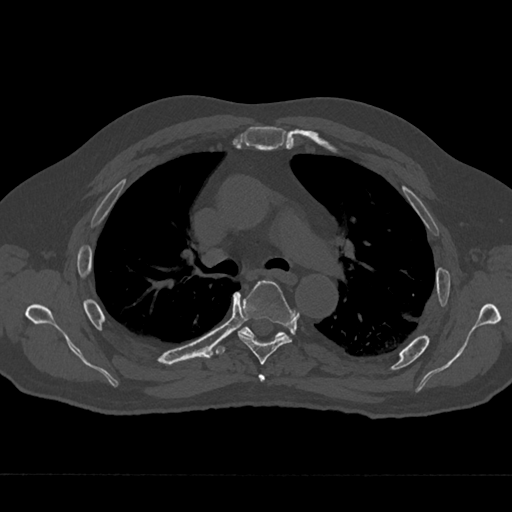
CT including the spine, one axial slice; slice 460 of 797 in the series (ordered by position); 120 kVp; bone window (W 1800 / L 400 HU); 0.5 mm slice thickness; 512 × 512 image matrix, field of view 377 × 377 mm. Patient: male, 75 years. From the clinical record (not read from this slice): primary cancer: renal; vertebrae with lytic lesions (as recorded): T4.
Structures marked on this image (semi-automatically segmented with operator editing):
- T4 vertebra: box from (x=258, y=374) to (x=265, y=382) px
- T5 vertebra: (x=238, y=281)–(x=294, y=365)
- T6 vertebra: (x=218, y=327)–(x=285, y=354)